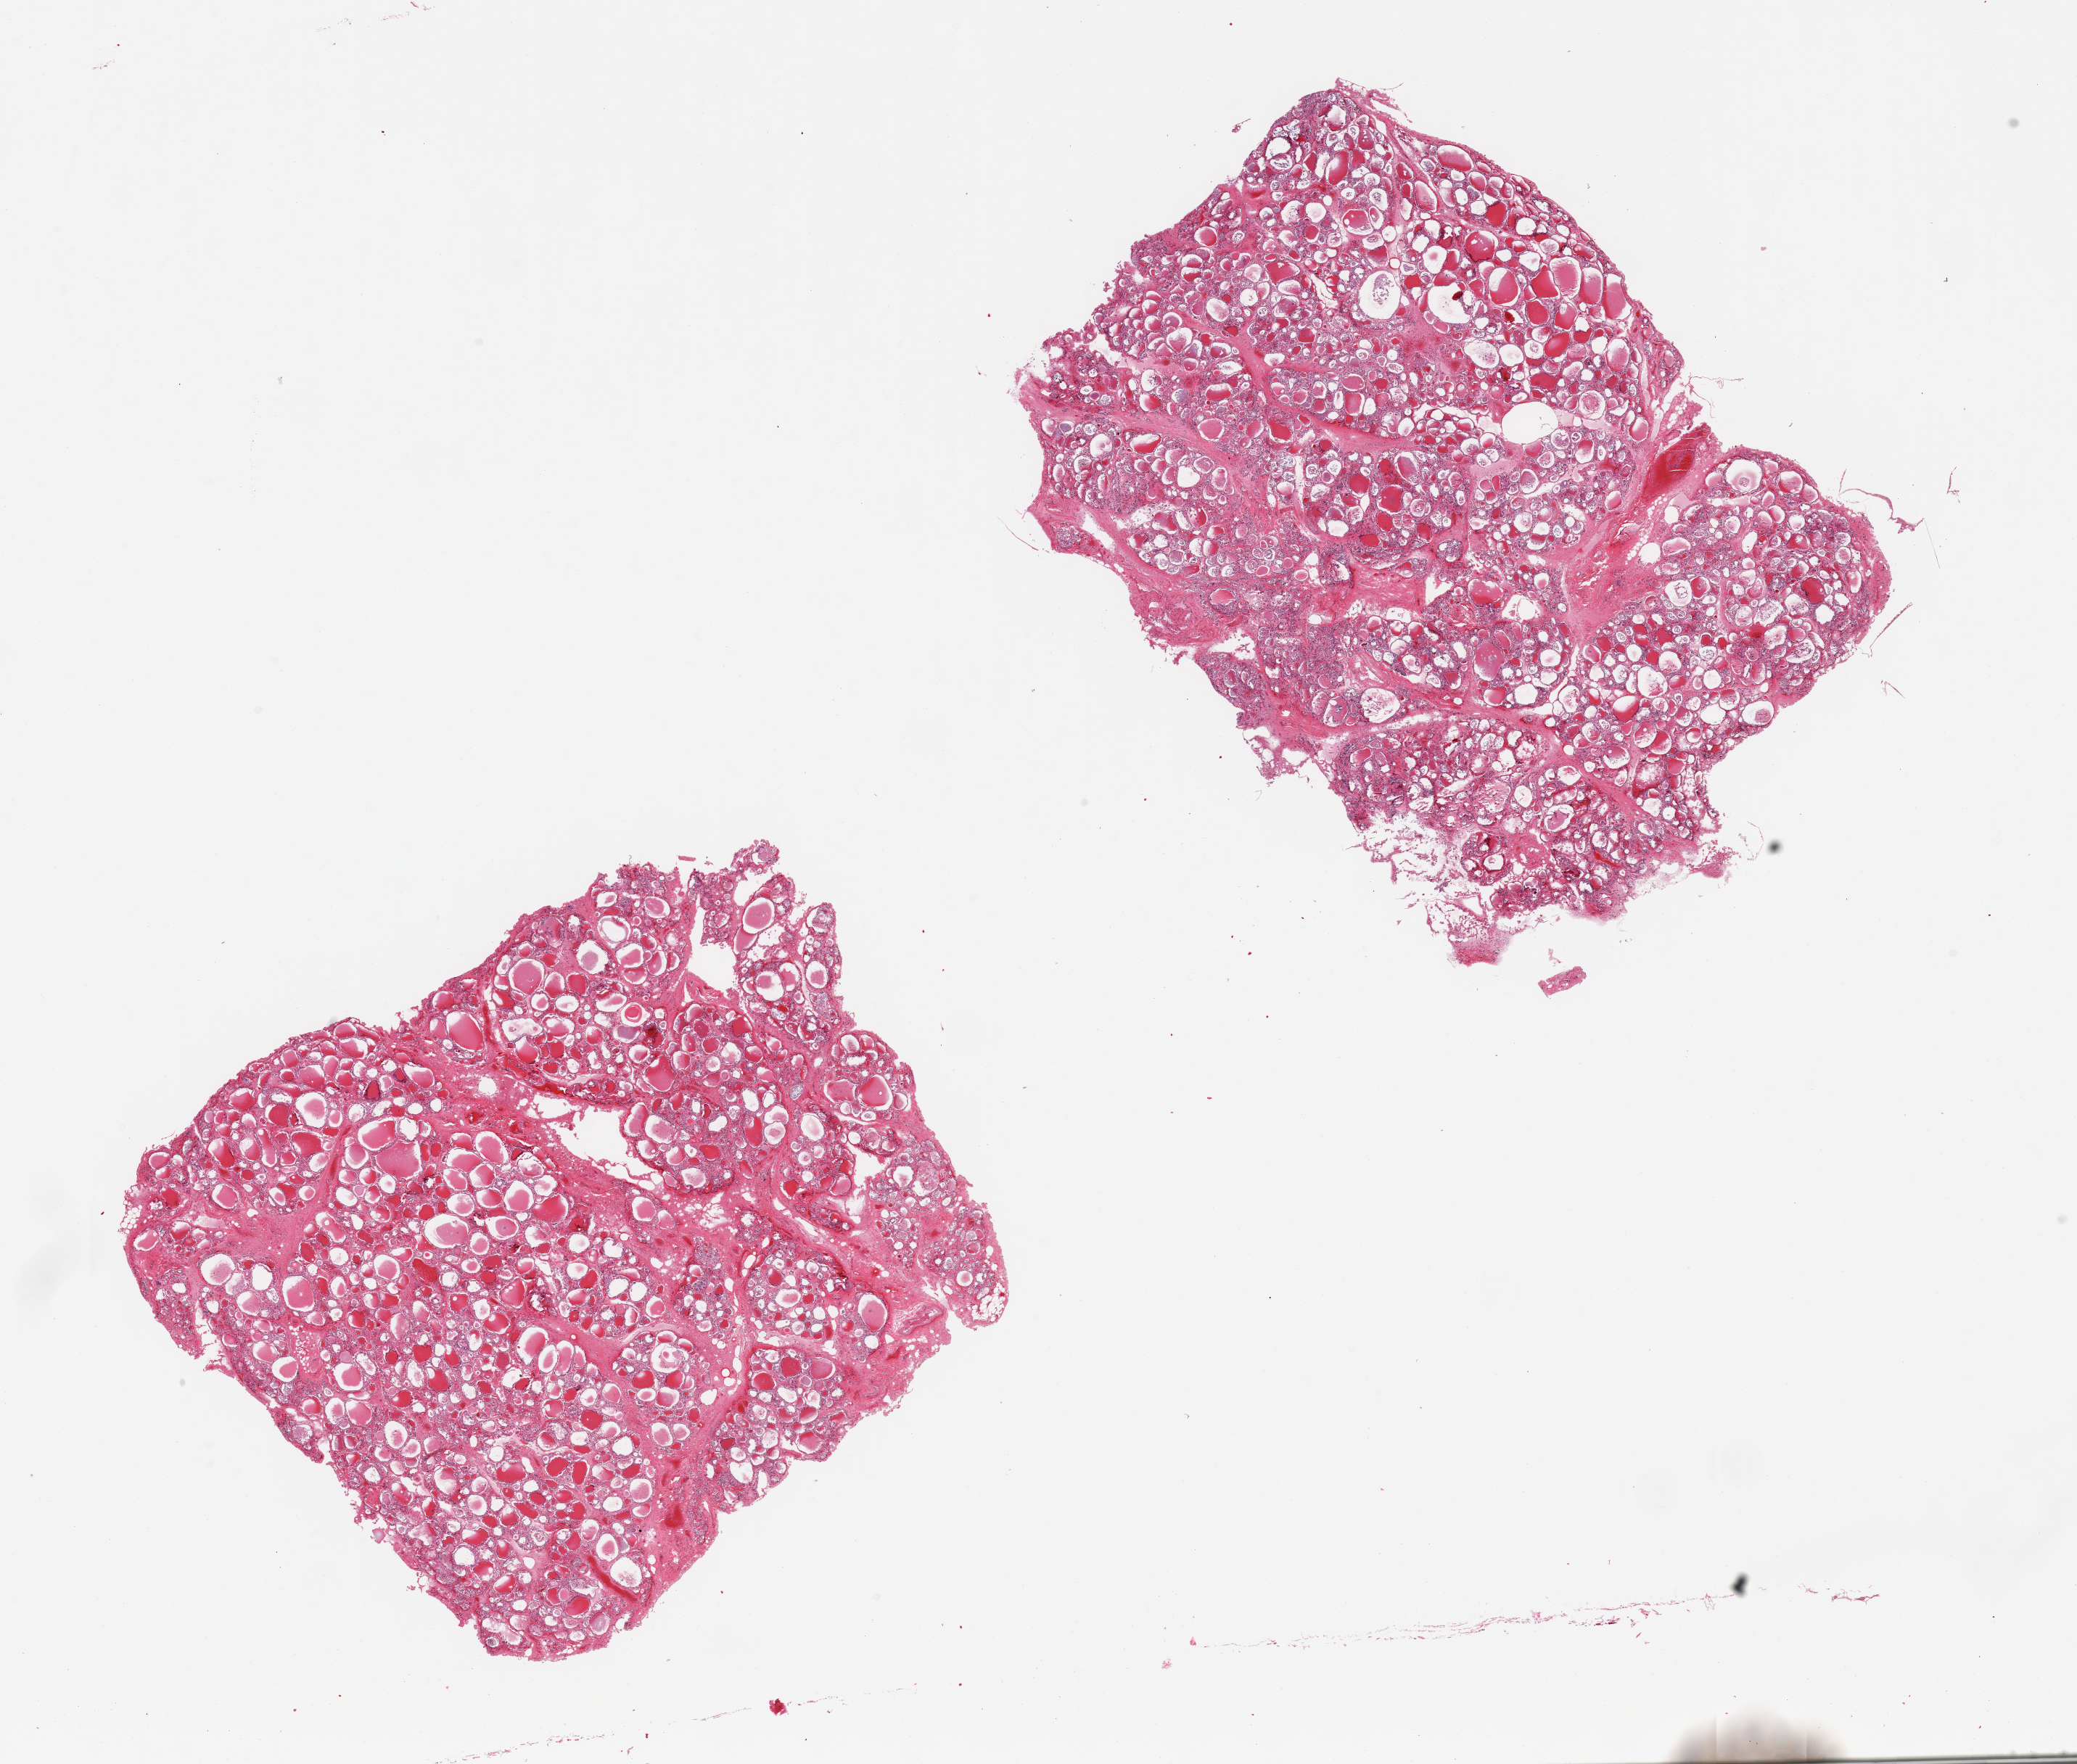
Whole-slide image, H&E stain, whole scanned area (about 22.6 x 19.2 mm, slide scanned at 20x) shown as a low-resolution overview. PAXgene-fixed paraffin-embedded (PFPE) section. Section of thyroid (target tissue). Donor tissue sample.
• pathologist's review note for this sample: 2 pieces; slightly nodular;, generally poor preservation, focally bordering on severe autolysis